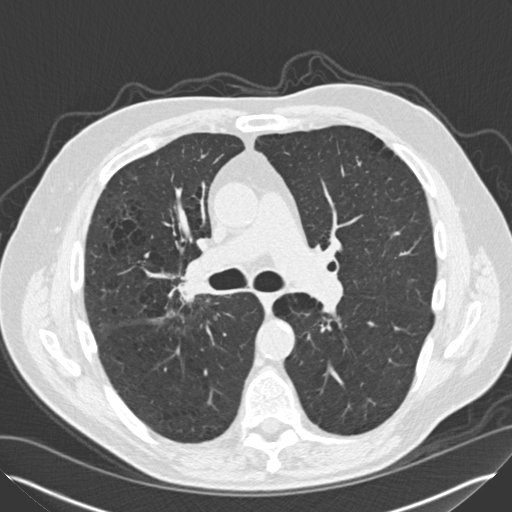
Low-dose screening chest CT, axial slice. Second screening round (one year after baseline). Lung window (W 1500 / L -600 HU). 2 mm slice thickness. 120 kVp. Slice 64 of 149 in the series. Male participant, aged 65 years at enrolment. Current smoker at enrolment.
• Lesion marked by an expert reader, bounding box (x1, y1, x2, y2) in pixels: (163, 261, 219, 315).
• The exam's reader record, not a measurement of the box and not confirmed to be the same lesion: non-calcified nodule or mass ≥4 mm, left lower lobe, 12 × 8 mm, smooth margins, soft tissue attenuation, pre-existing on the prior screen: yes; interval growth: yes.
• Note: the box lies in the patient's right hemithorax on this image, whereas the reader's record names the left lung; they may be different findings.
• Participant outcome: lung cancer diagnosed 67 days after this screen — non-small cell carcinoma, left lower lobe, right hilum, poorly differentiated (G3), stage IV (AJCC 6th edition), 5 mm at pathology.